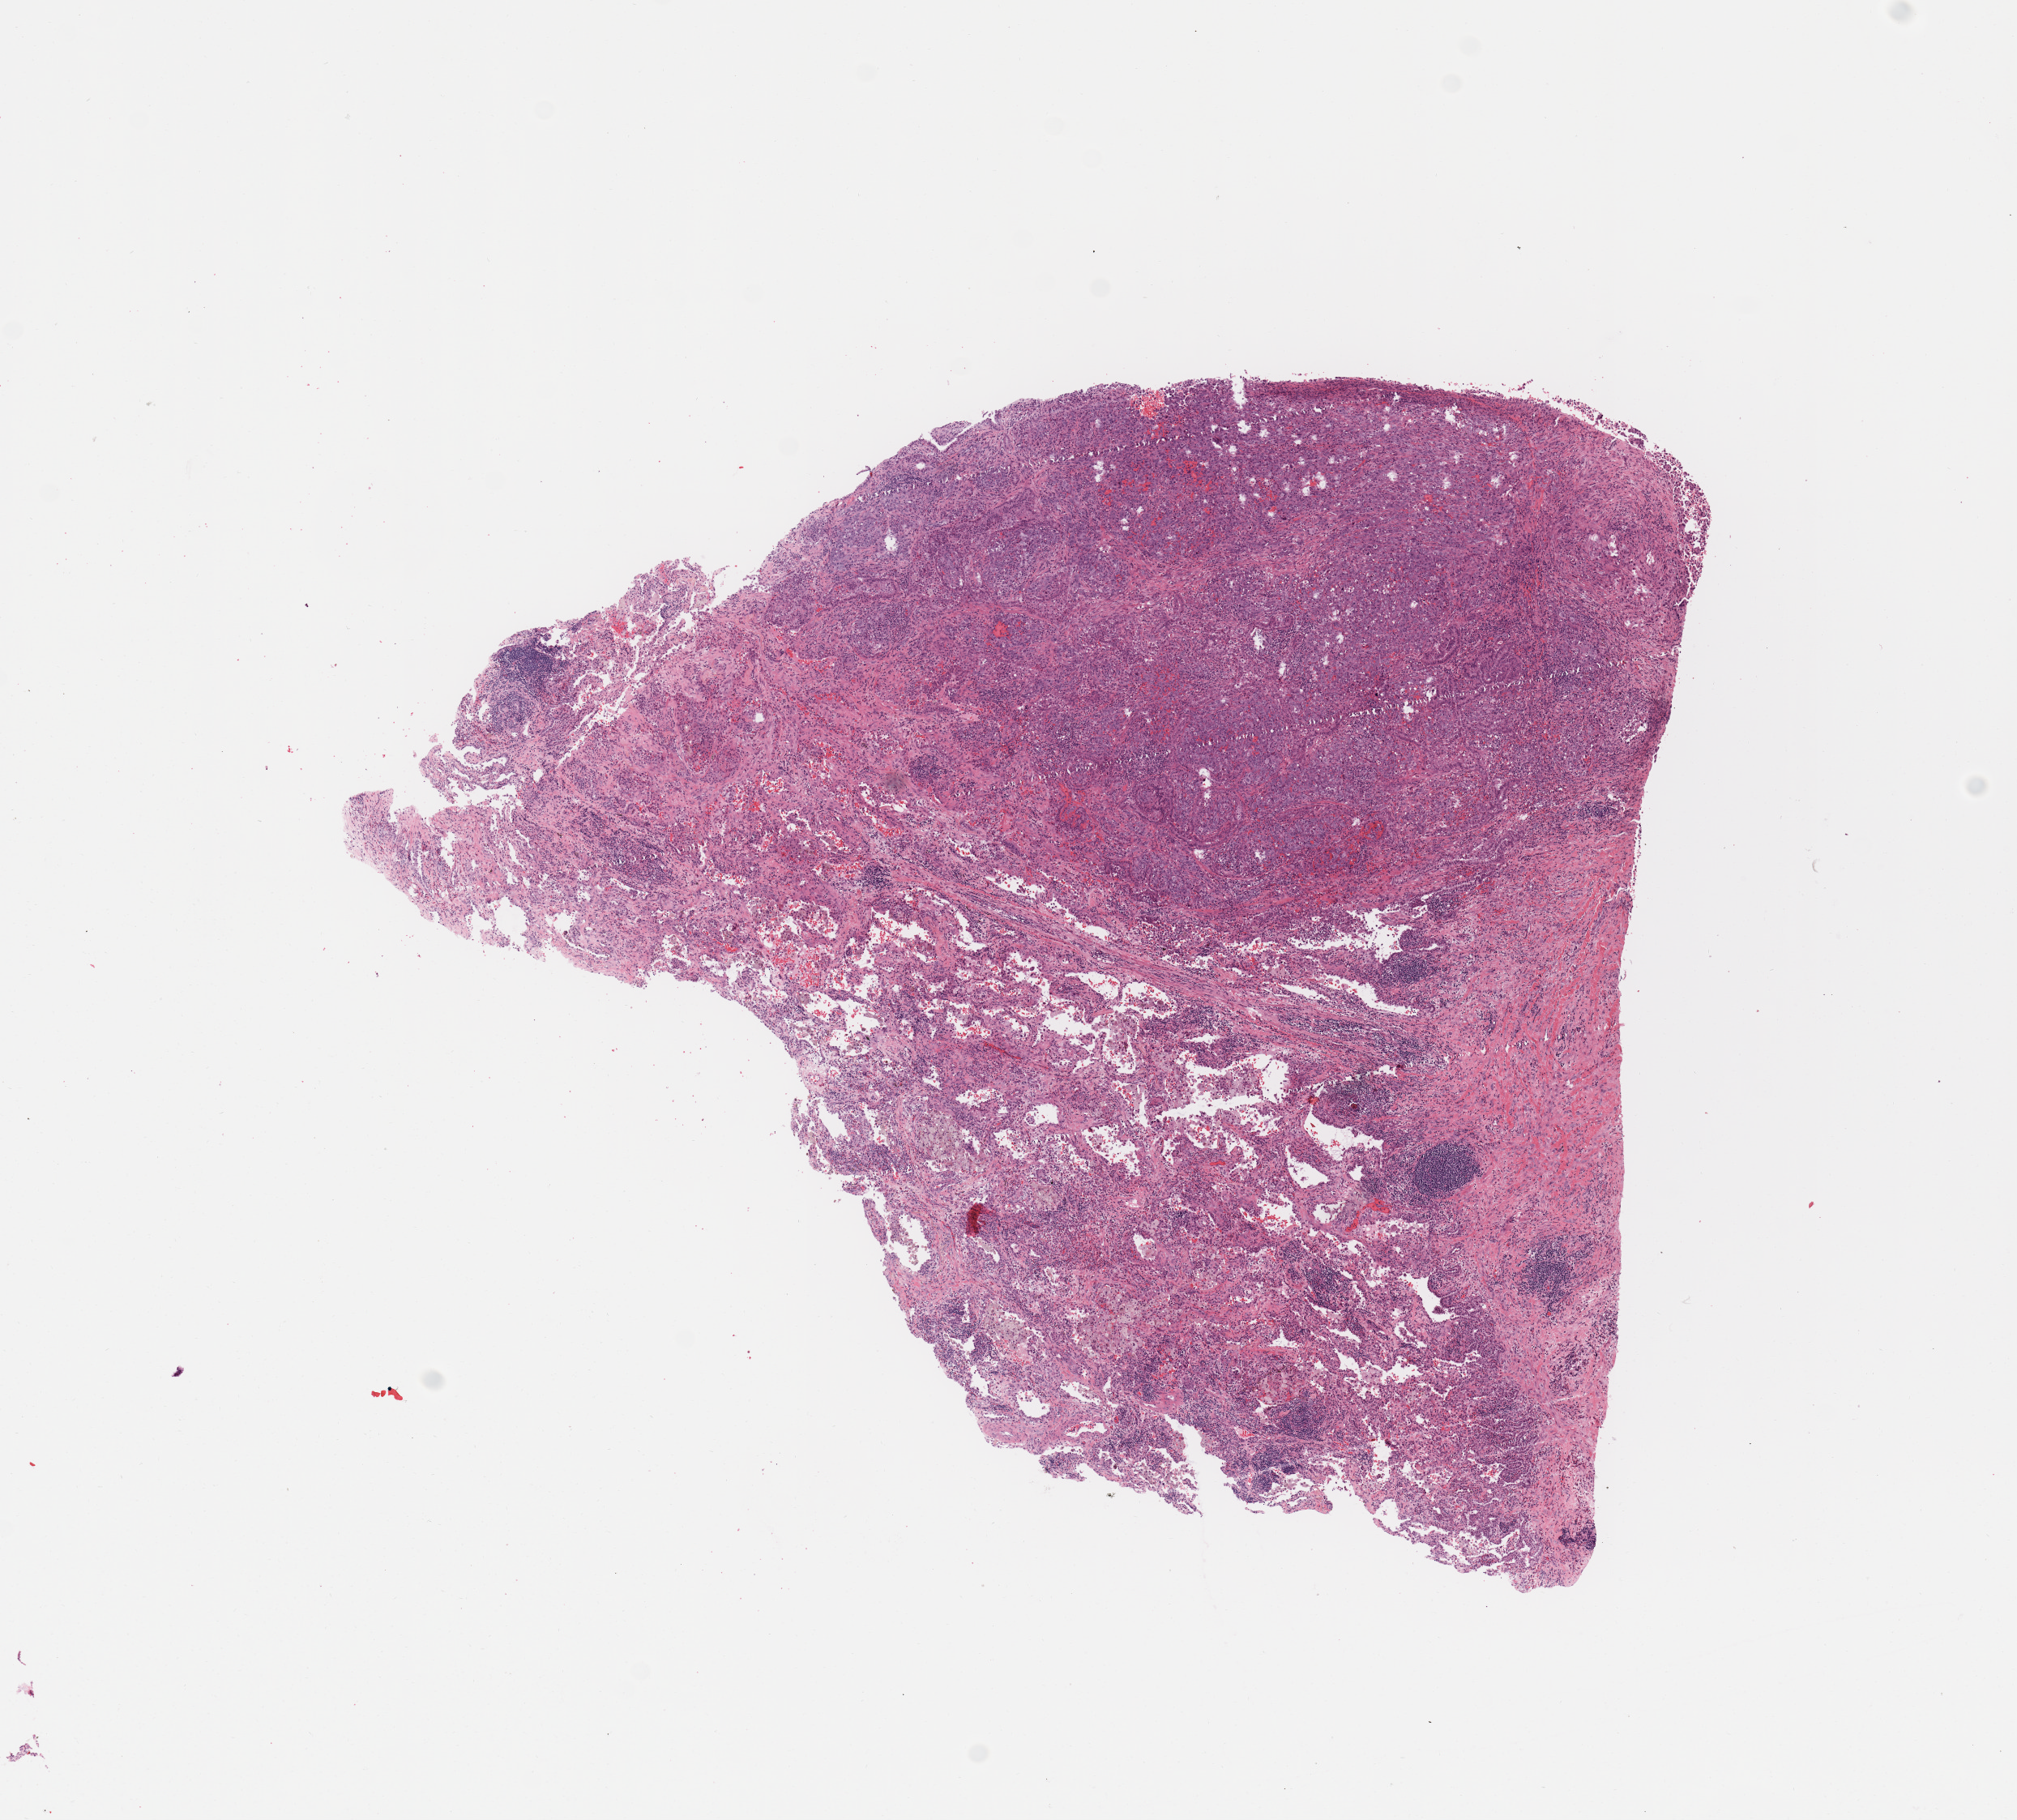
Digitized H&E-stained tissue section (whole slide) — a low-resolution overview of the entire scanned area, about 9.8 x 8.9 mm (slide scanned at 20x); tumour tissue sample, lung. Patient: male, age 62 years.
Diagnosis: Adenocarcinoma, NOS.